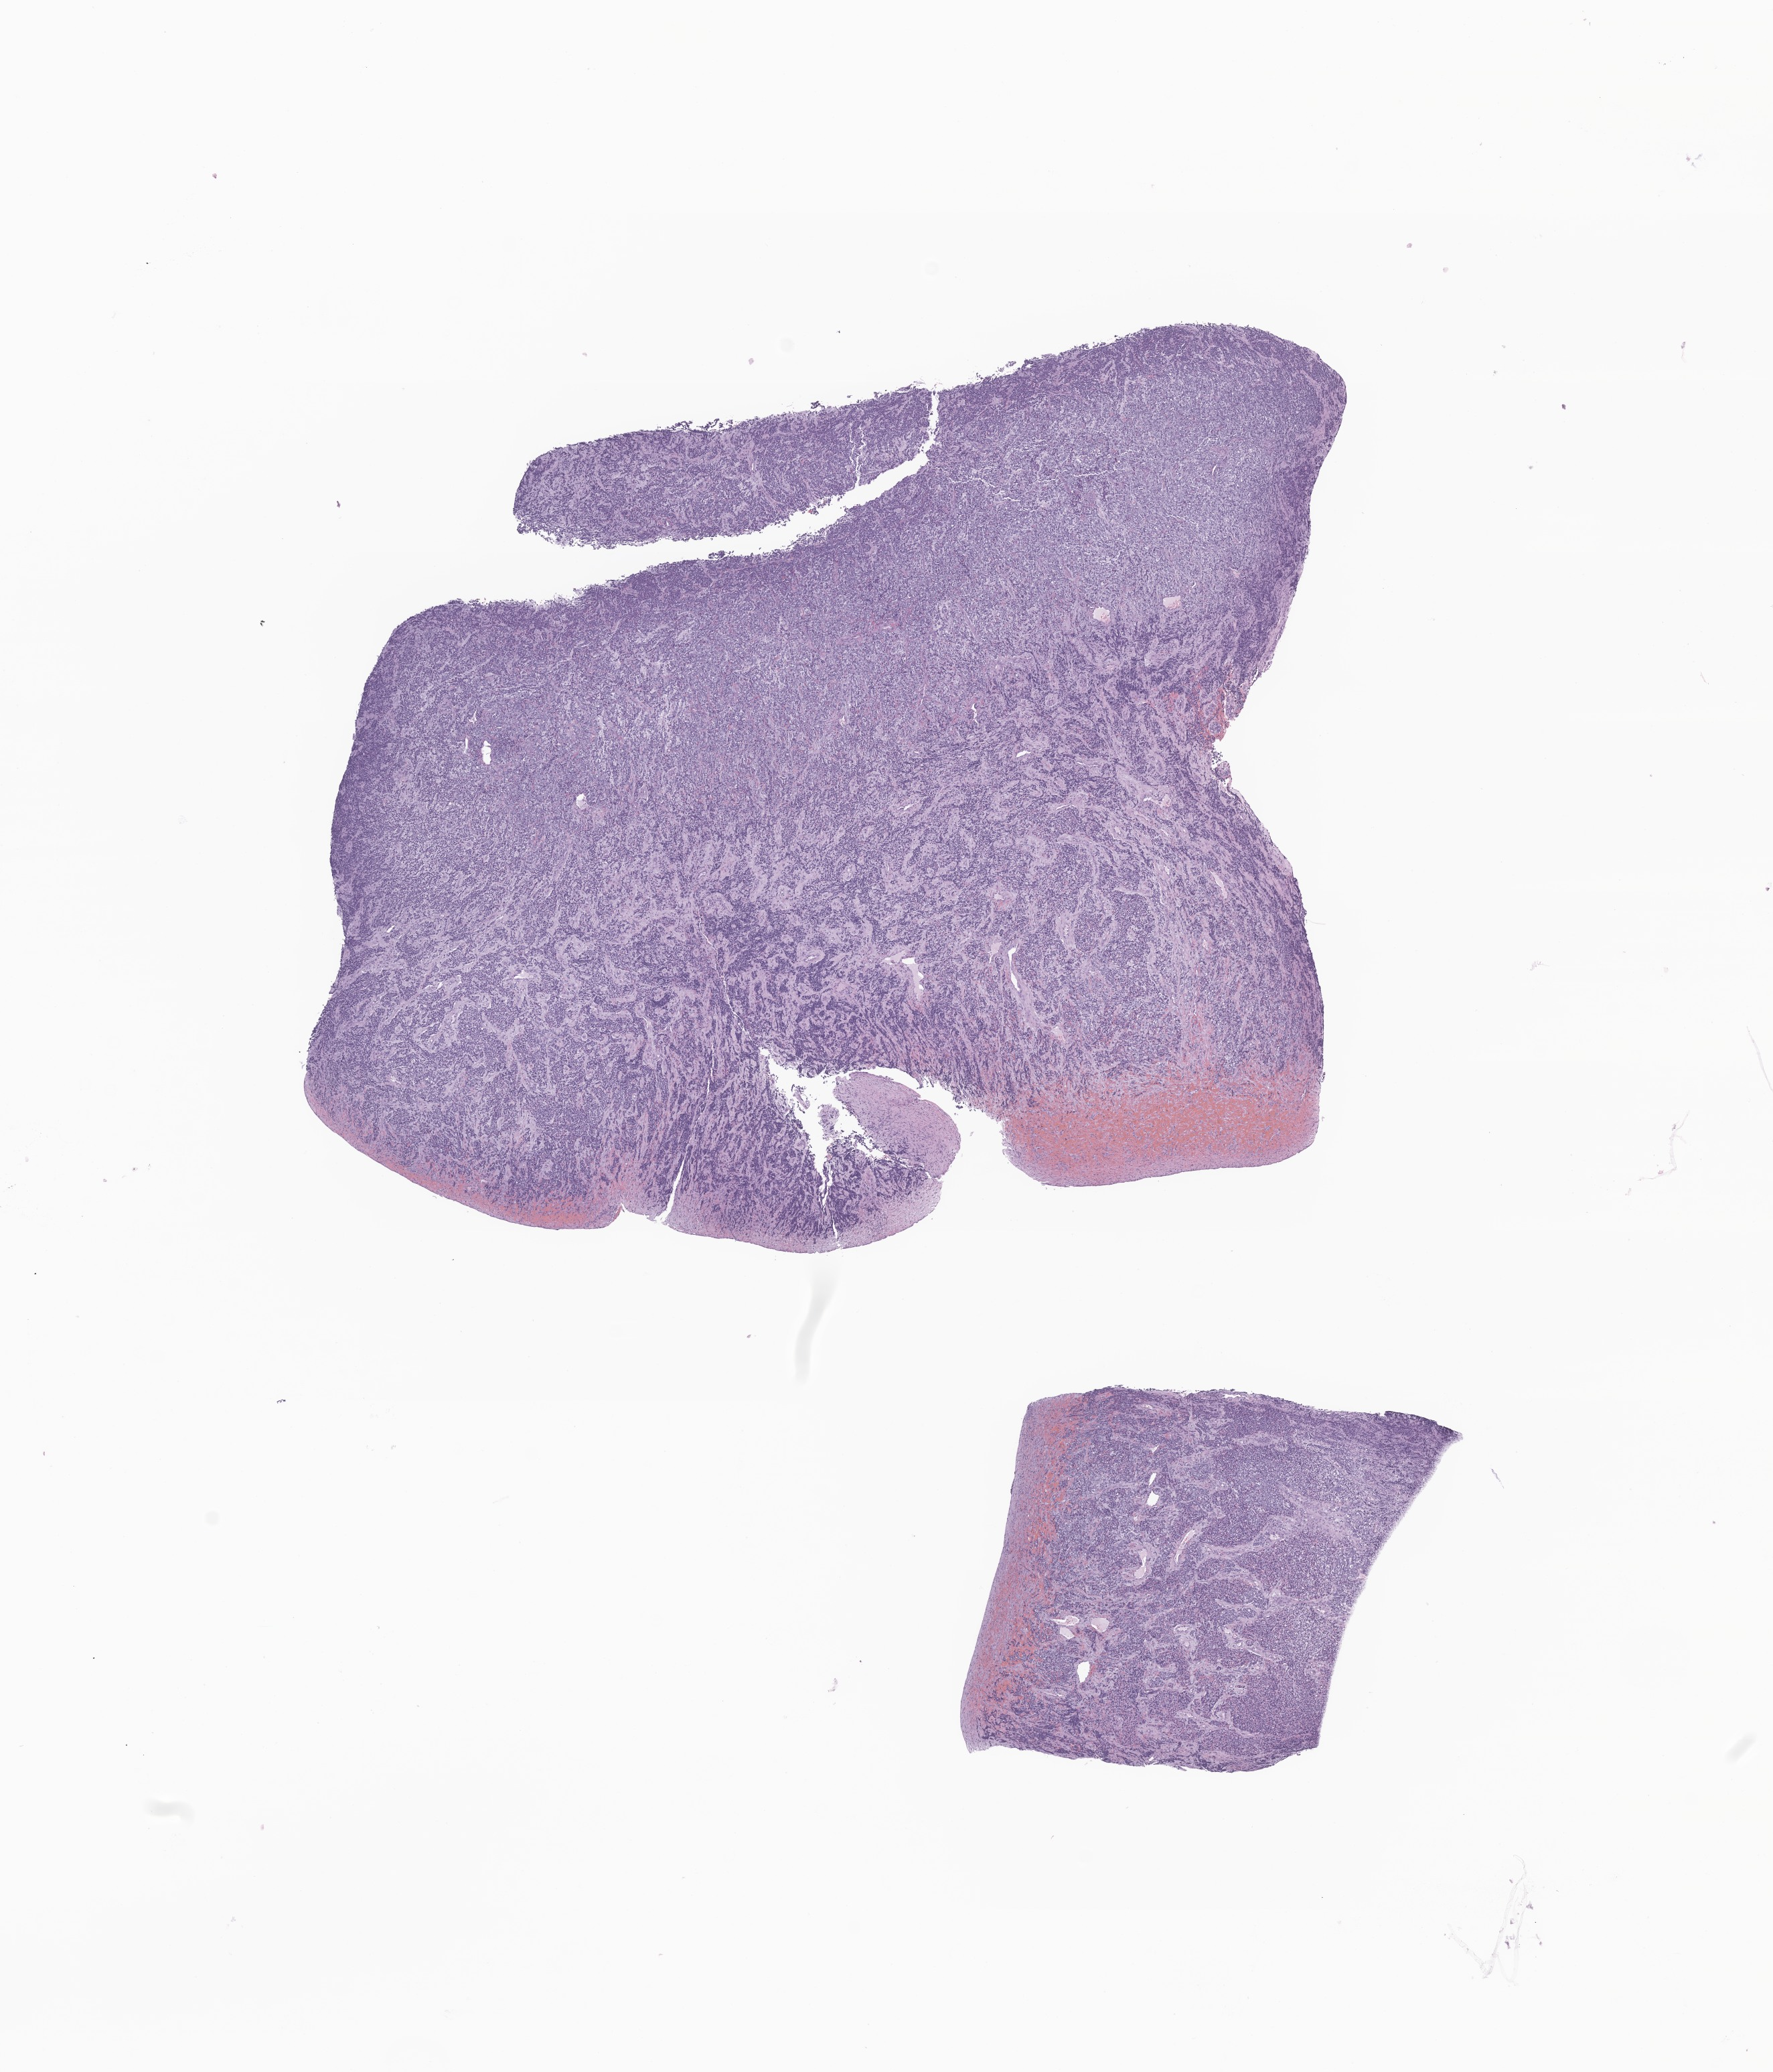
Whole-slide image, haematoxylin and eosin stain of tumor tissue from the abdomen, shown as a low-resolution overview of the whole scanned area (about 11.2 x 13.0 mm); formalin-fixed, paraffin-embedded (FFPE) tissue. Male patient, age 590 days.
Diagnosis: Neuroblastoma, NOS.